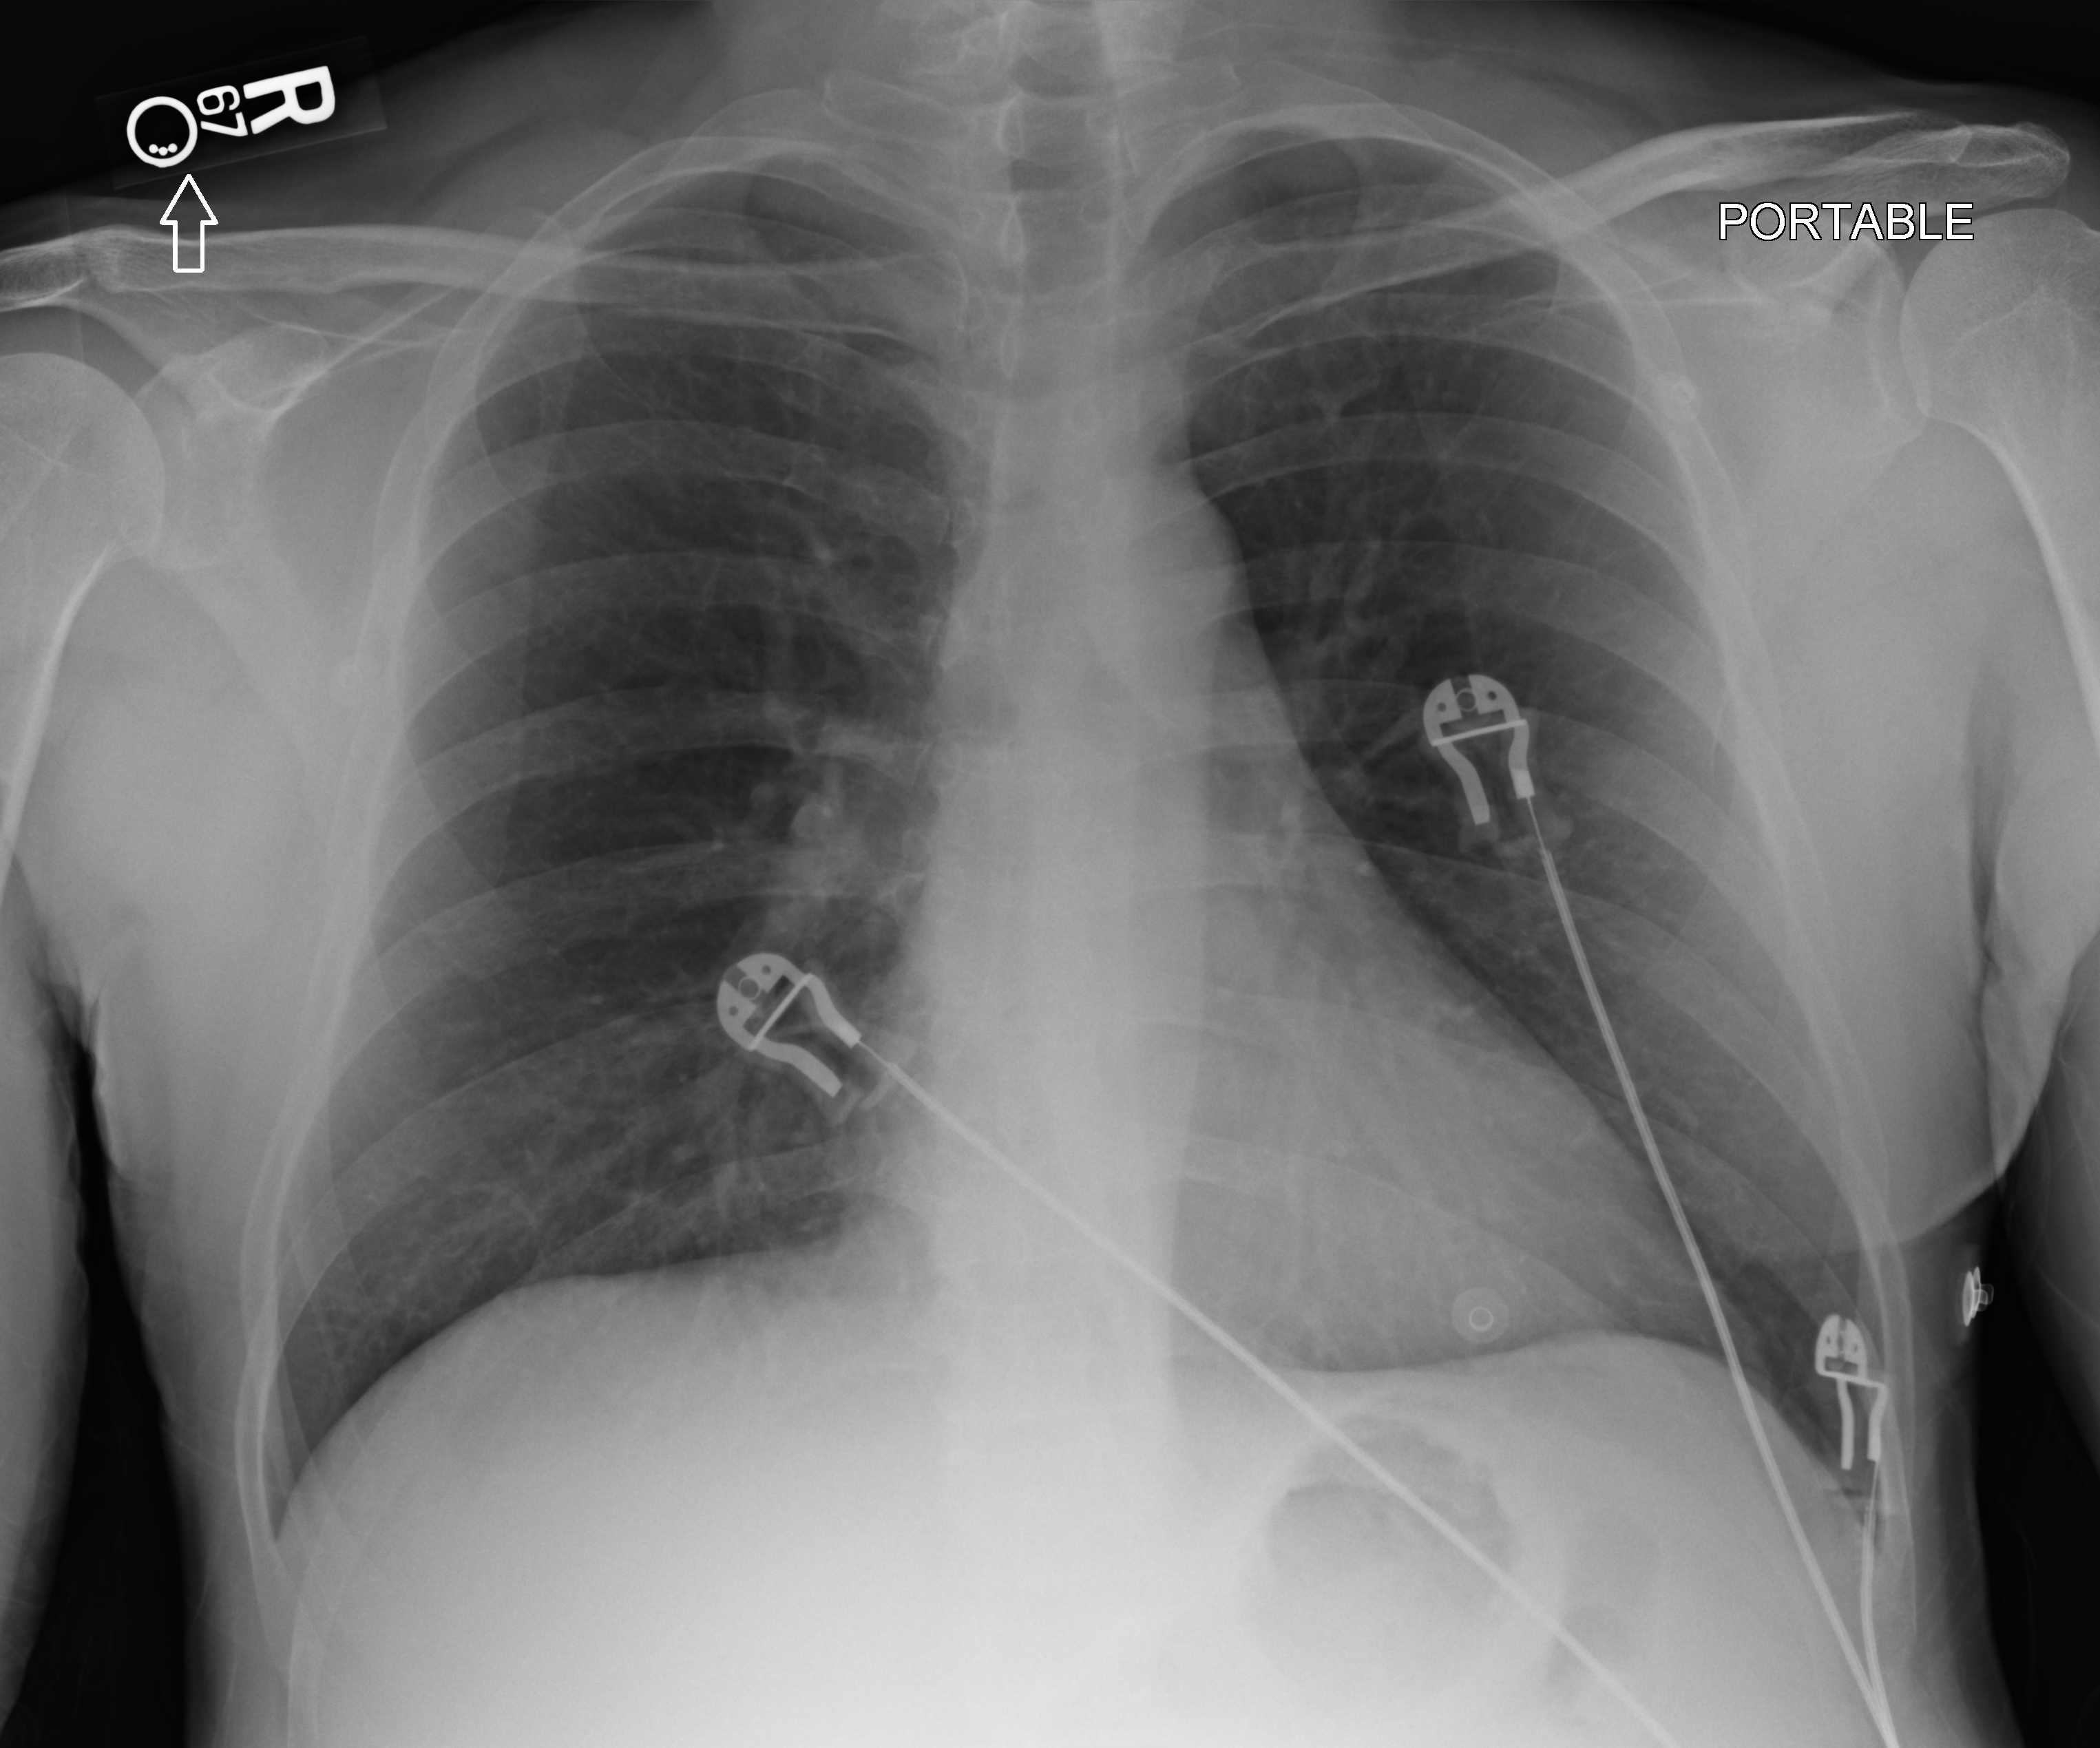
Portable chest radiograph; anteroposterior (AP) projection. Male patient hospitalised with COVID-19, age 18–59 years.
Admission-level facts for this patient (not findings on this image; timing relative to this image not recorded):
- admitted to intensive care during this hospital stay: no
- mechanically ventilated during this hospital stay: no